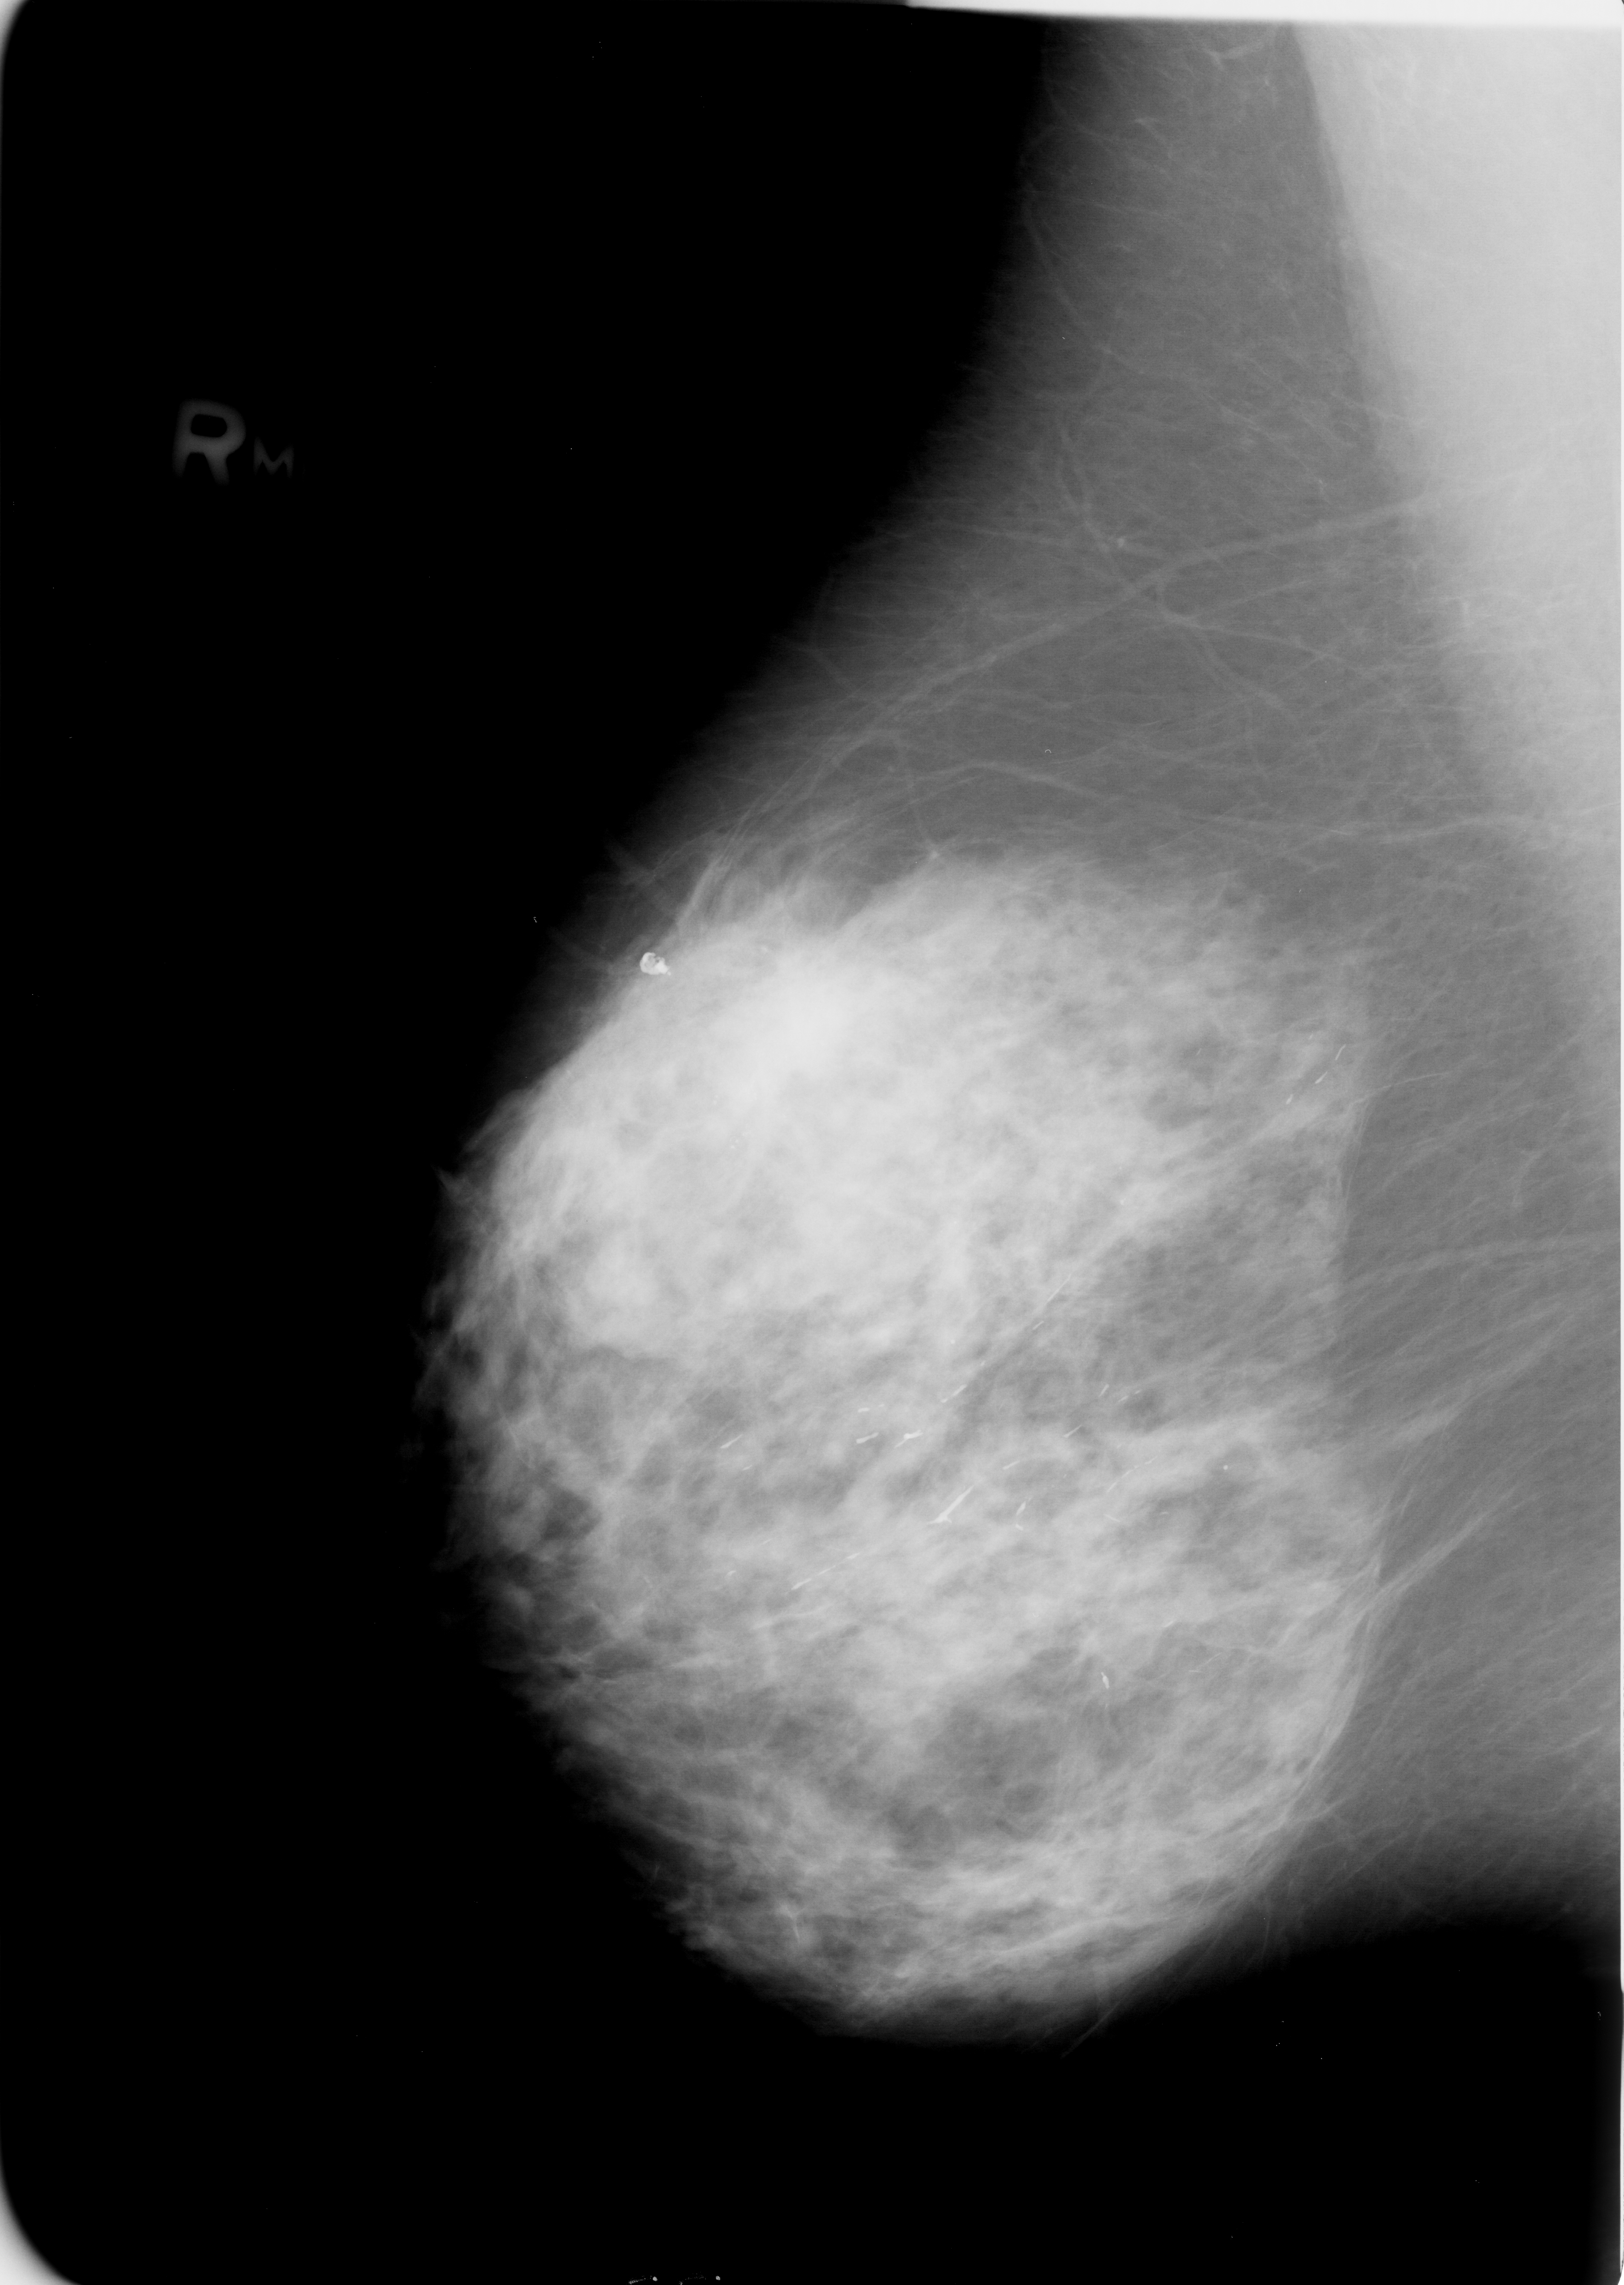
Mammogram (digitized film). Right breast. Mediolateral oblique (MLO) view. BI-RADS breast density category 3 (scale 1–4). 1624 × 2285 image matrix.
Expert-marked regions of interest on this film, with their recorded descriptors:
- mass, shape irregular / architectural distortion, margins obscured / ill defined / spiculated; BI-RADS assessment category 4; subtlety rating 3 on a 1 (subtle) to 5 (obvious) scale; pathology (as recorded): malignant: box from (x=741, y=964) to (x=855, y=1095) px